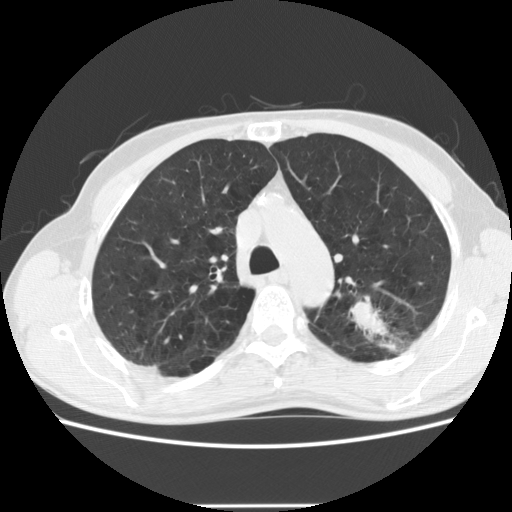
Low-dose screening chest CT, one axial slice; position 141 of 191 along the scan axis; reconstruction kernel STANDARD; lung window (W 1500 / L -600 HU); 512 × 512 image matrix, field of view 352 × 352 mm.
Outlined on this slice (expert manual segmentation):
- lesion 1 (tumor, upper lobe of left lung): box from (x=351, y=301) to (x=387, y=336) px